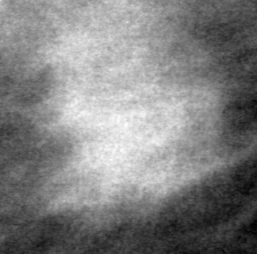
Cropped region of a digitized screen-film mammogram centred on a radiologist-marked abnormality, left breast, MLO view.
Finding: mass, shape irregular, margins spiculated; BI-RADS assessment category 5; pathology result (as recorded, not read from the image): malignant.